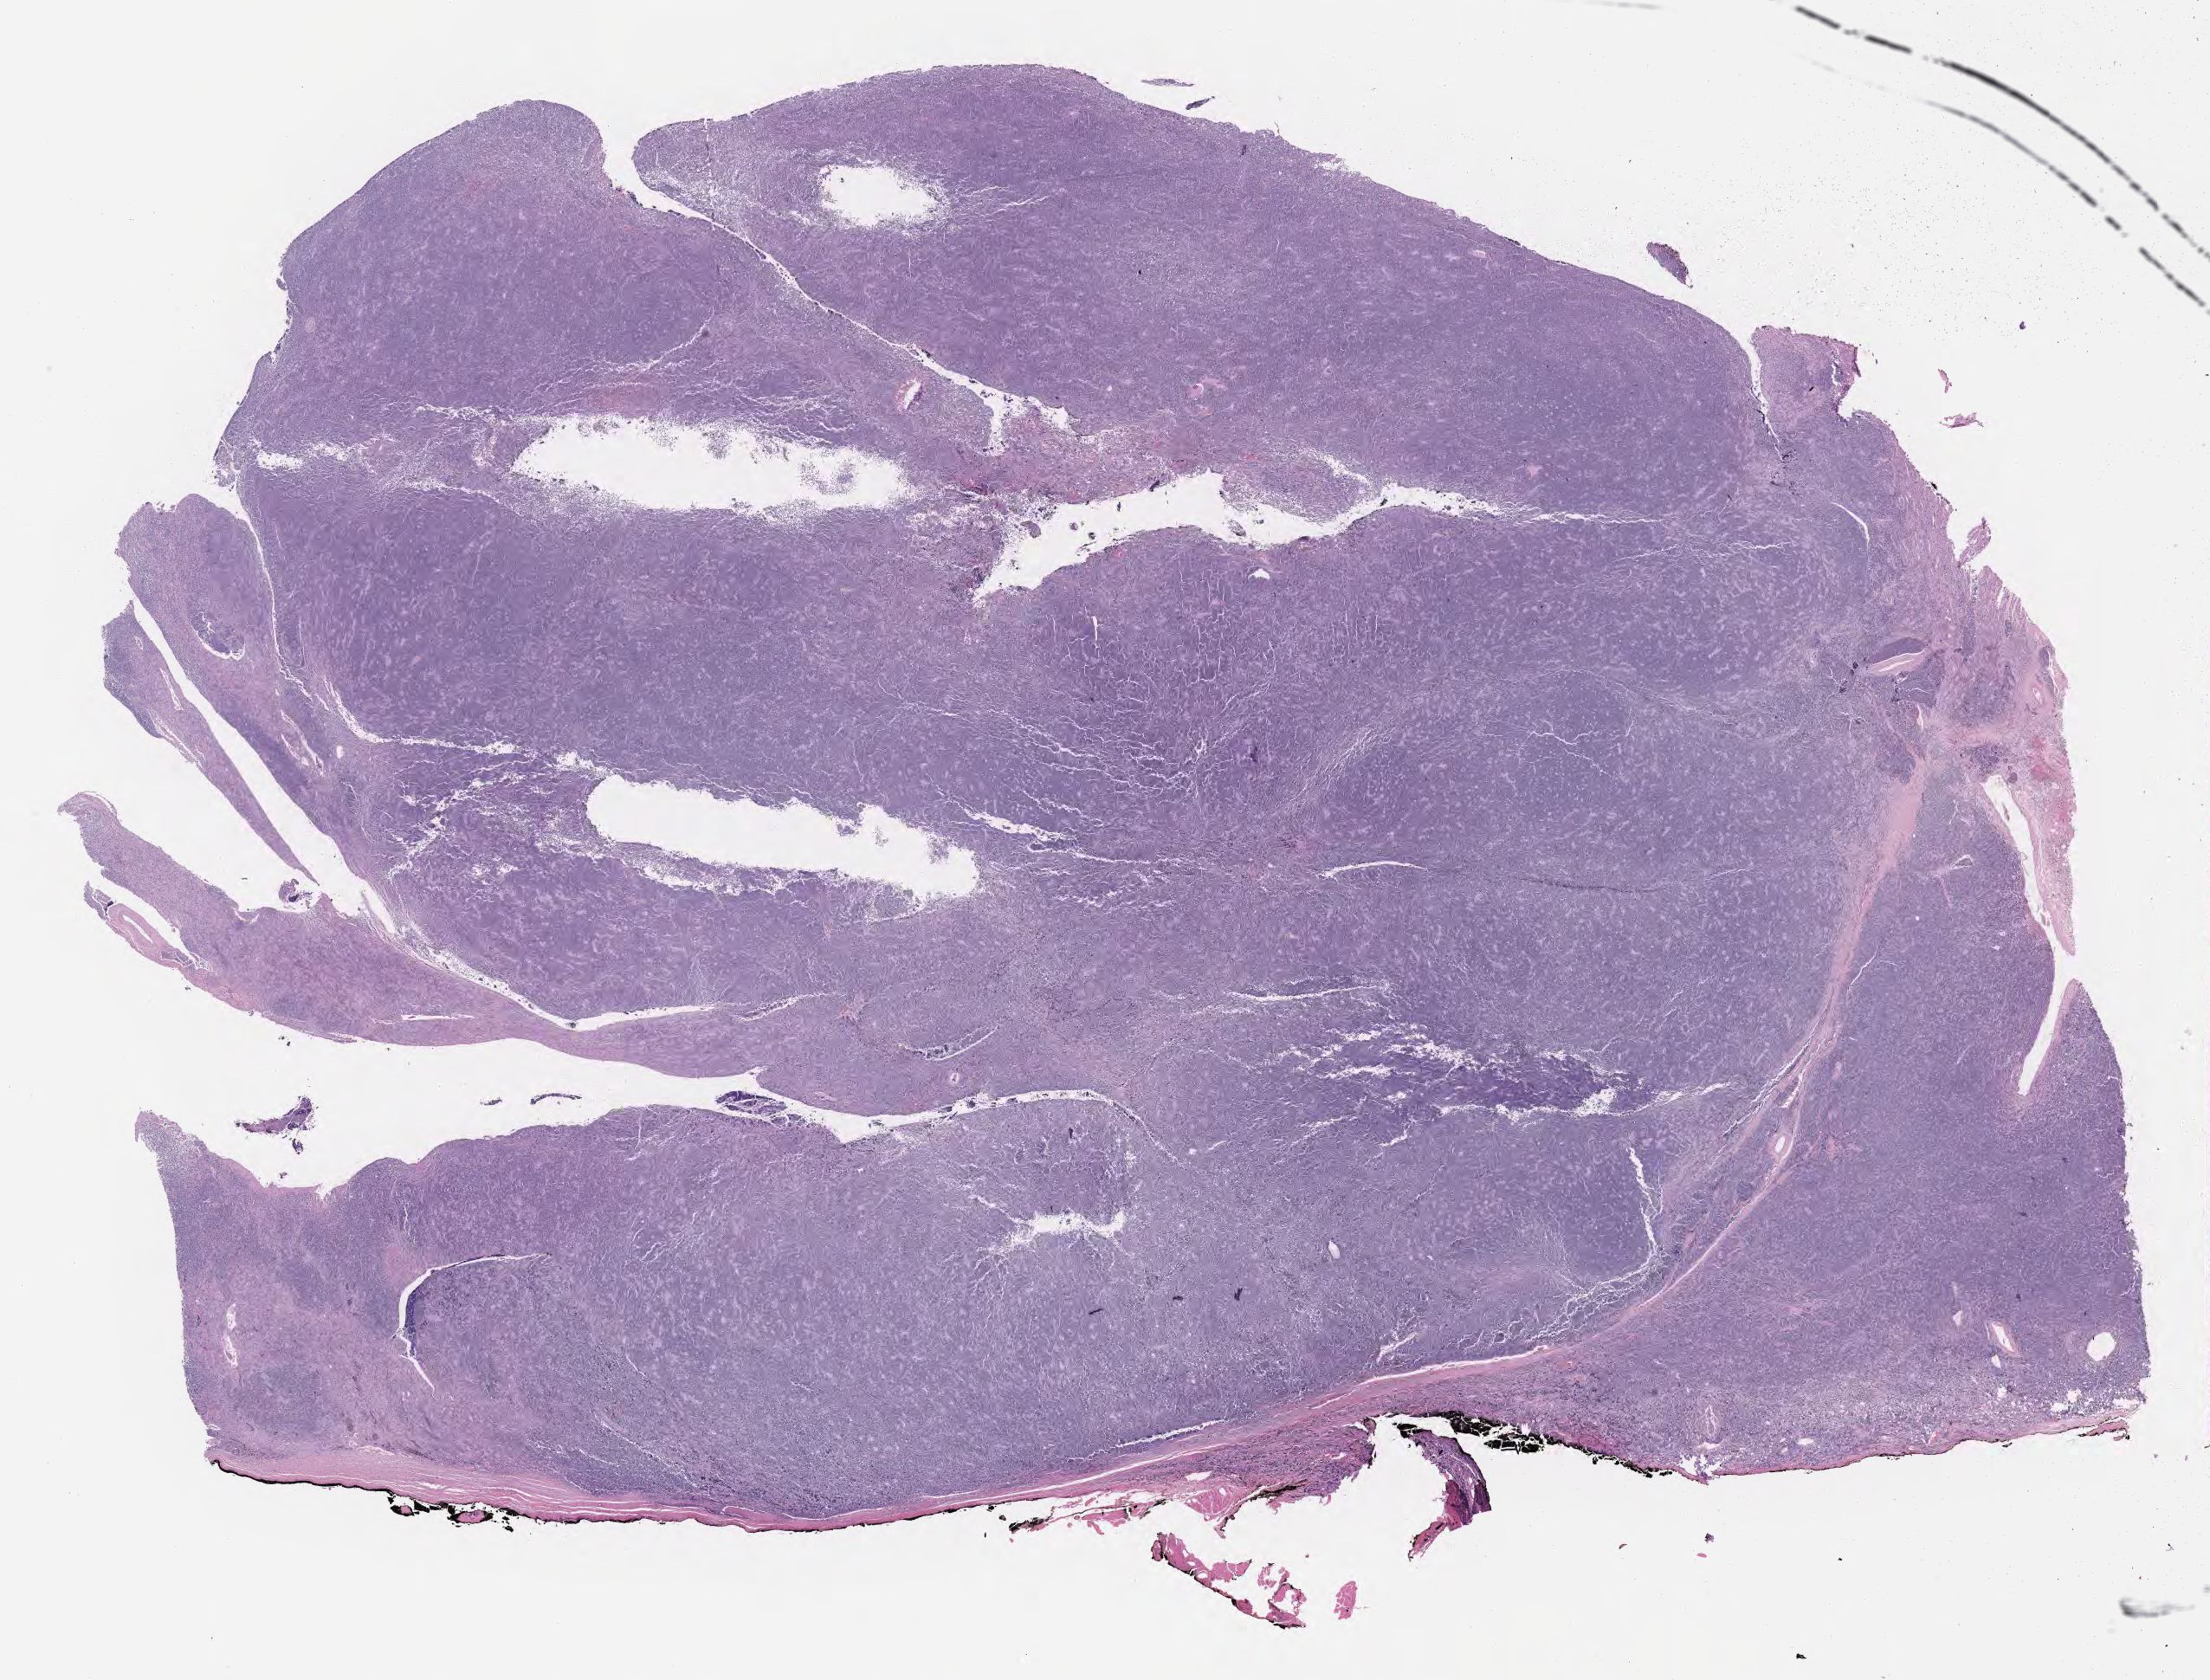
Digitized hematoxylin and eosin (H&E)-stained section — low-resolution overview of the scanned area, about 20.6 x 15.7 mm; specimen: tumor tissue; anatomic site: skin of lower limb. Patient male; 53 years old.
Histologic diagnosis: Neoplasm, uncertain whether benign or malignant.